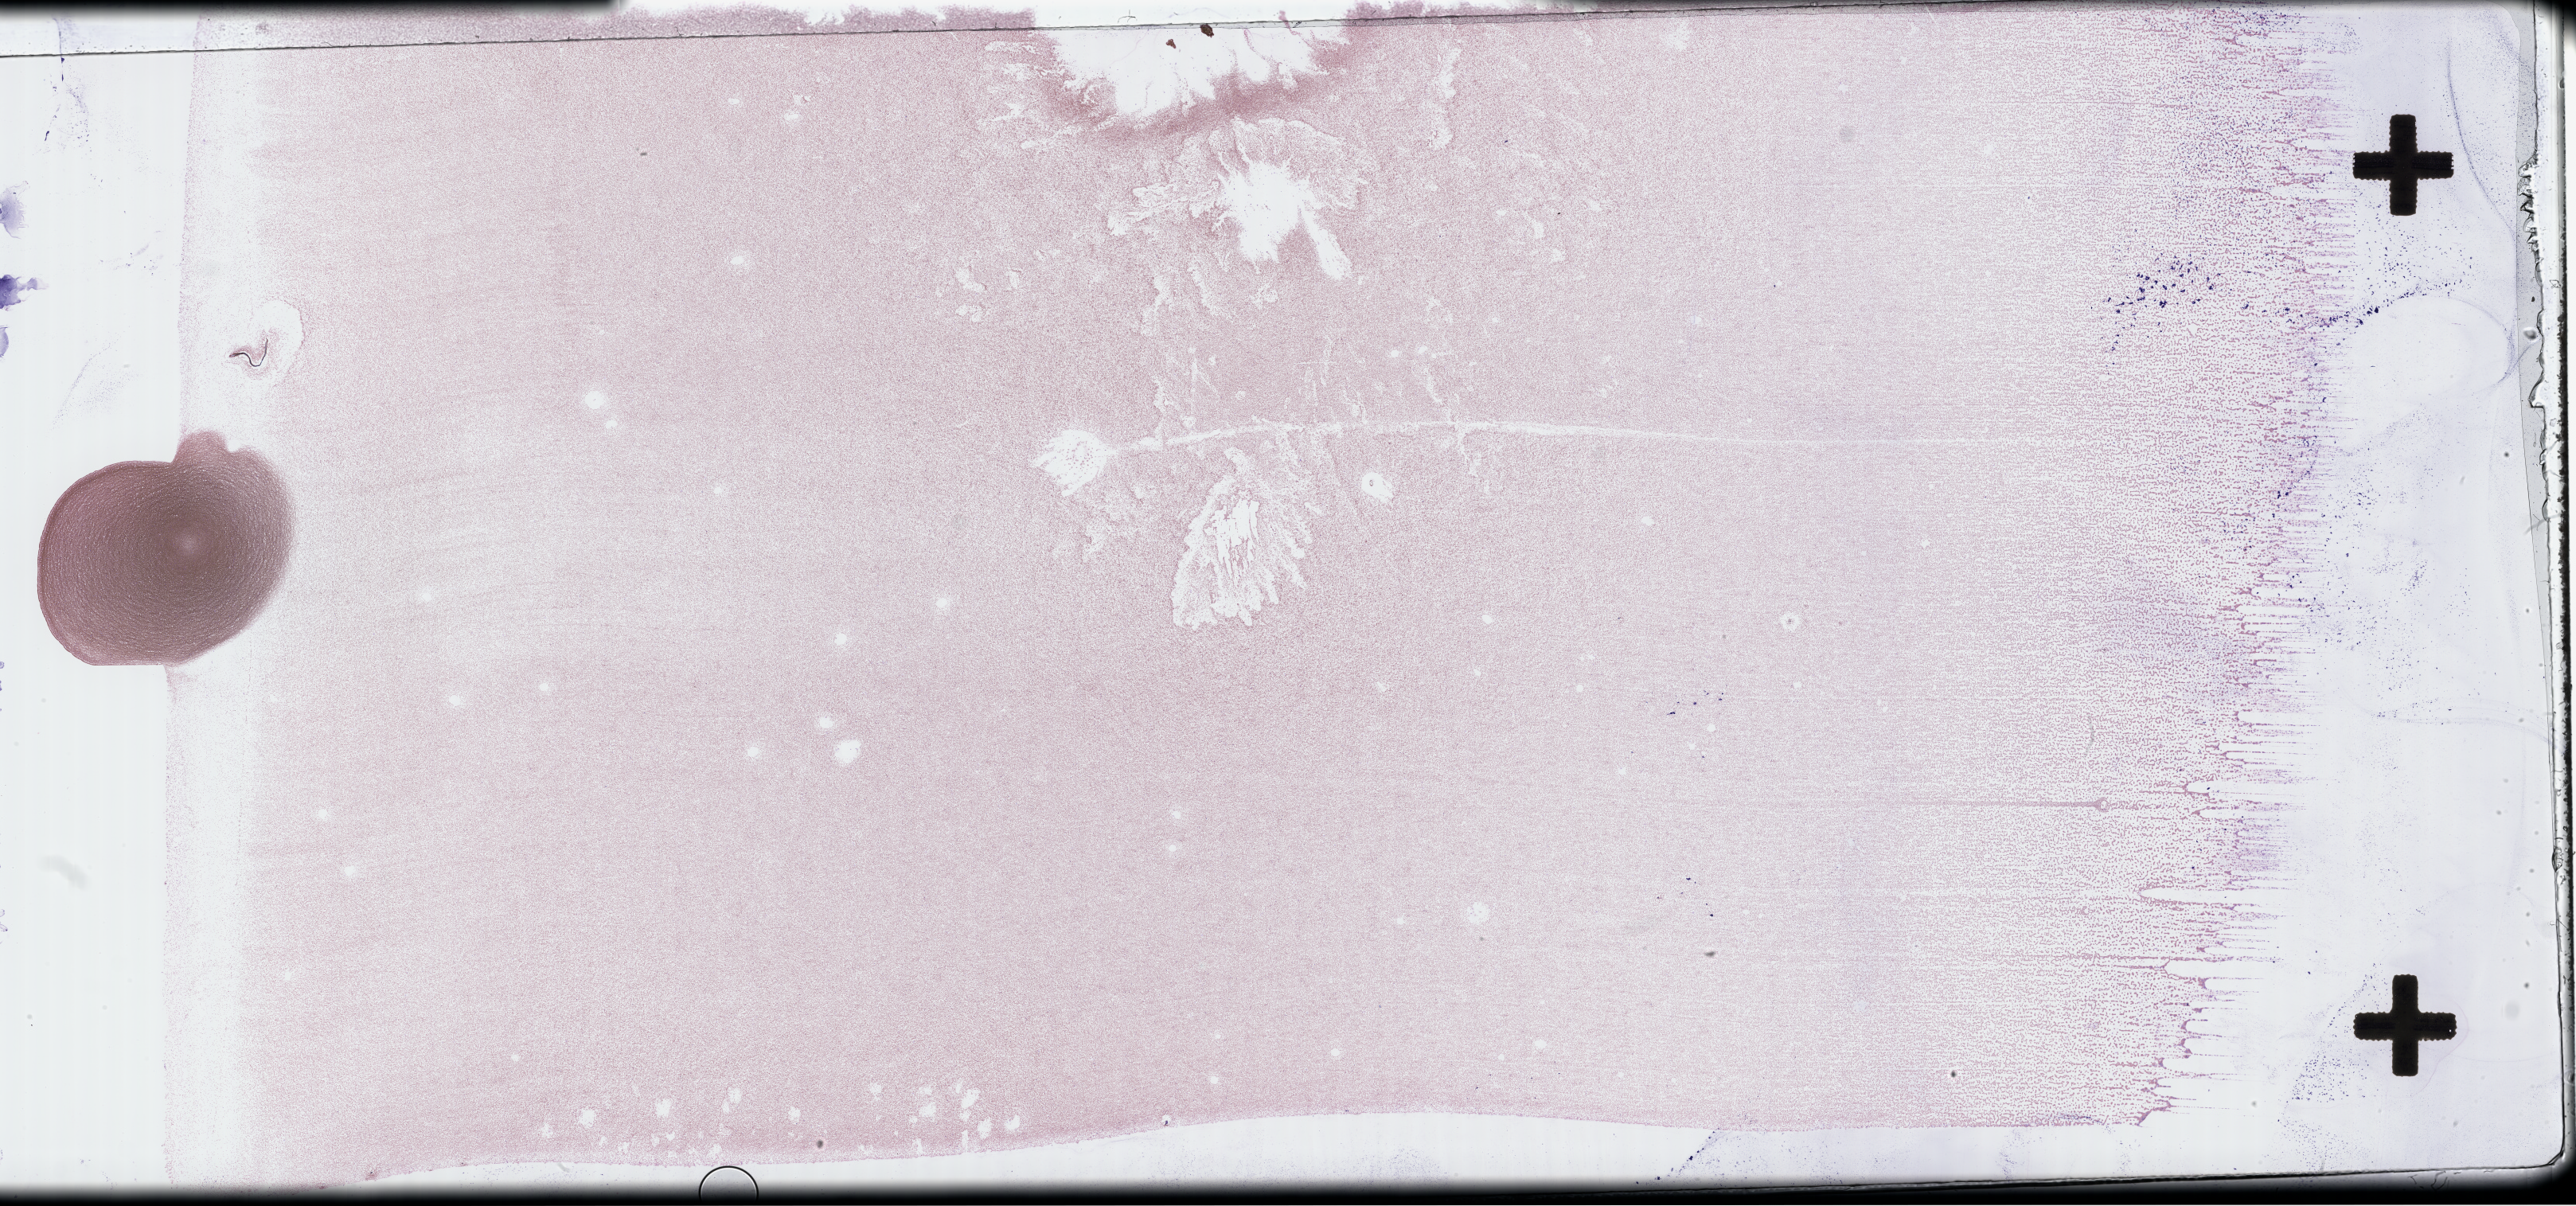
Wright–Giemsa-stained bone marrow smear, whole-slide image, shown as a low-resolution overview of the whole scanned area (about 52.3 x 24.5 mm). Patient: male.
Patient diagnosis: Plasma Cell Myeloma.